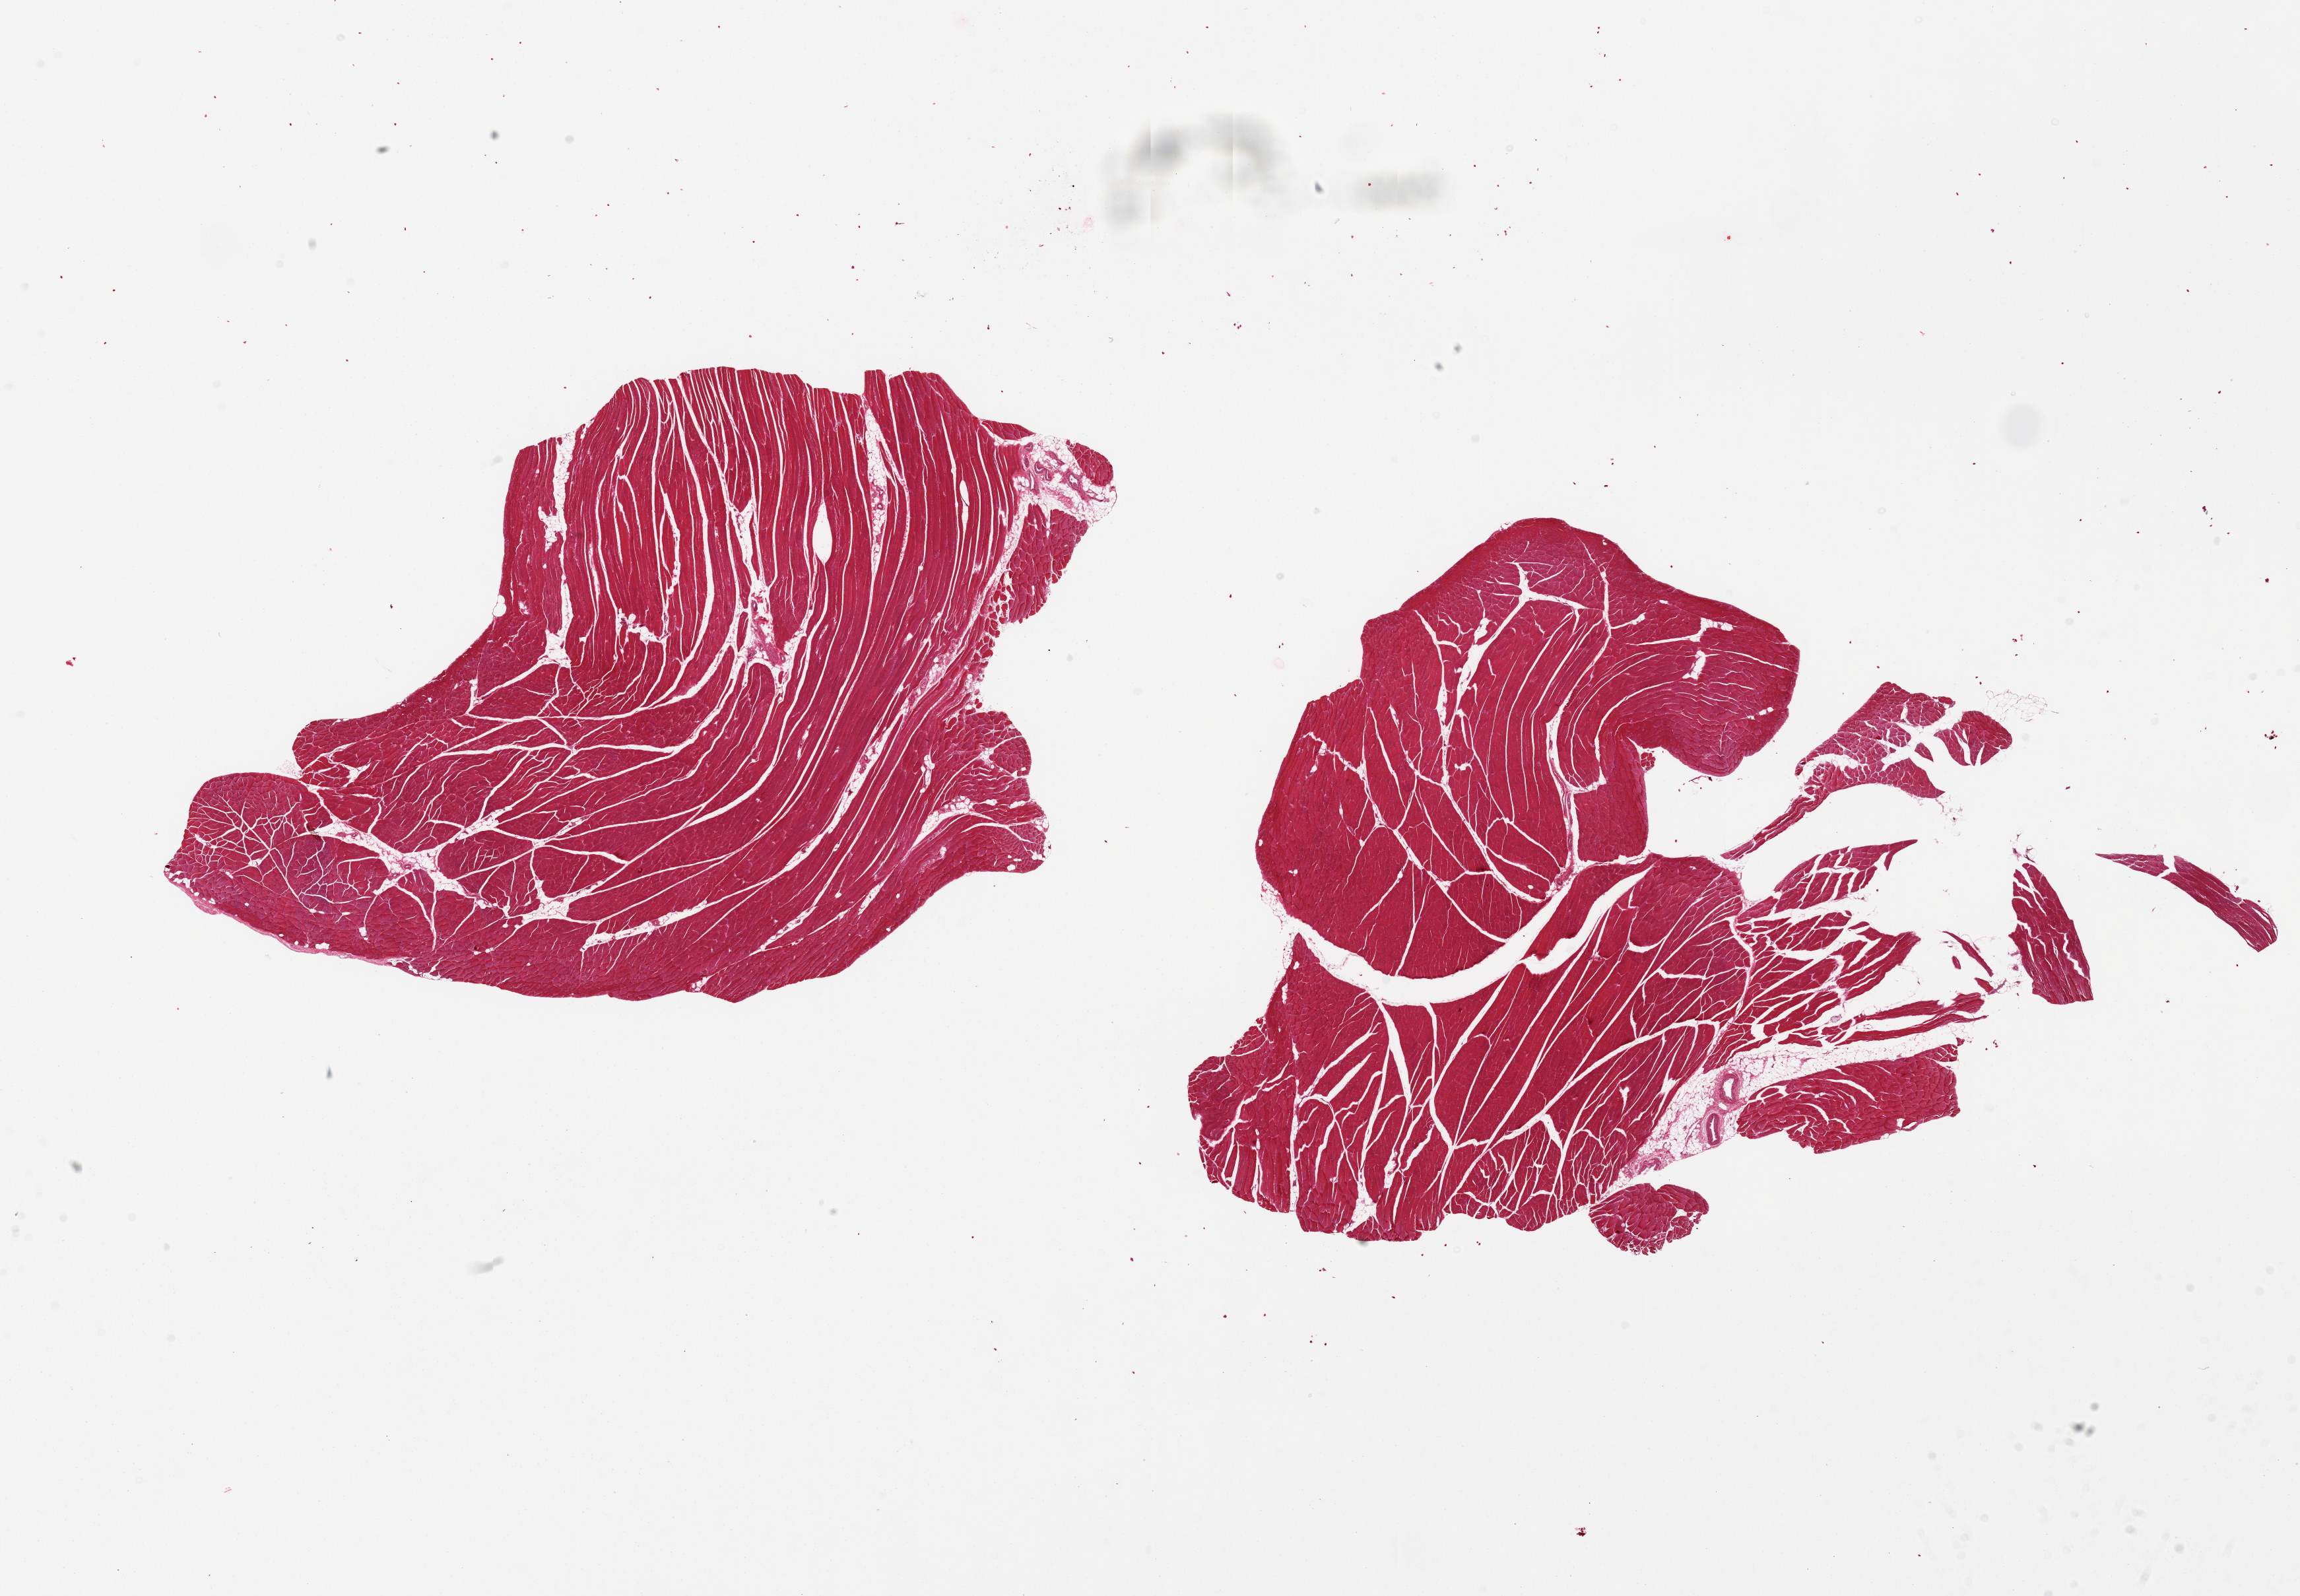
H&E whole-slide image, shown as a low-resolution overview of the whole scanned area (about 27.6 x 19.1 mm, from a 20x scan); PAXgene-fixed, paraffin-embedded tissue; sampled site (target tissue): skeletal muscle; donor tissue sample.
• reviewer comment on this tissue sample: 2 pieces. 10.5x9 & 13x9mm; Very well trimmed of extraneous tissue